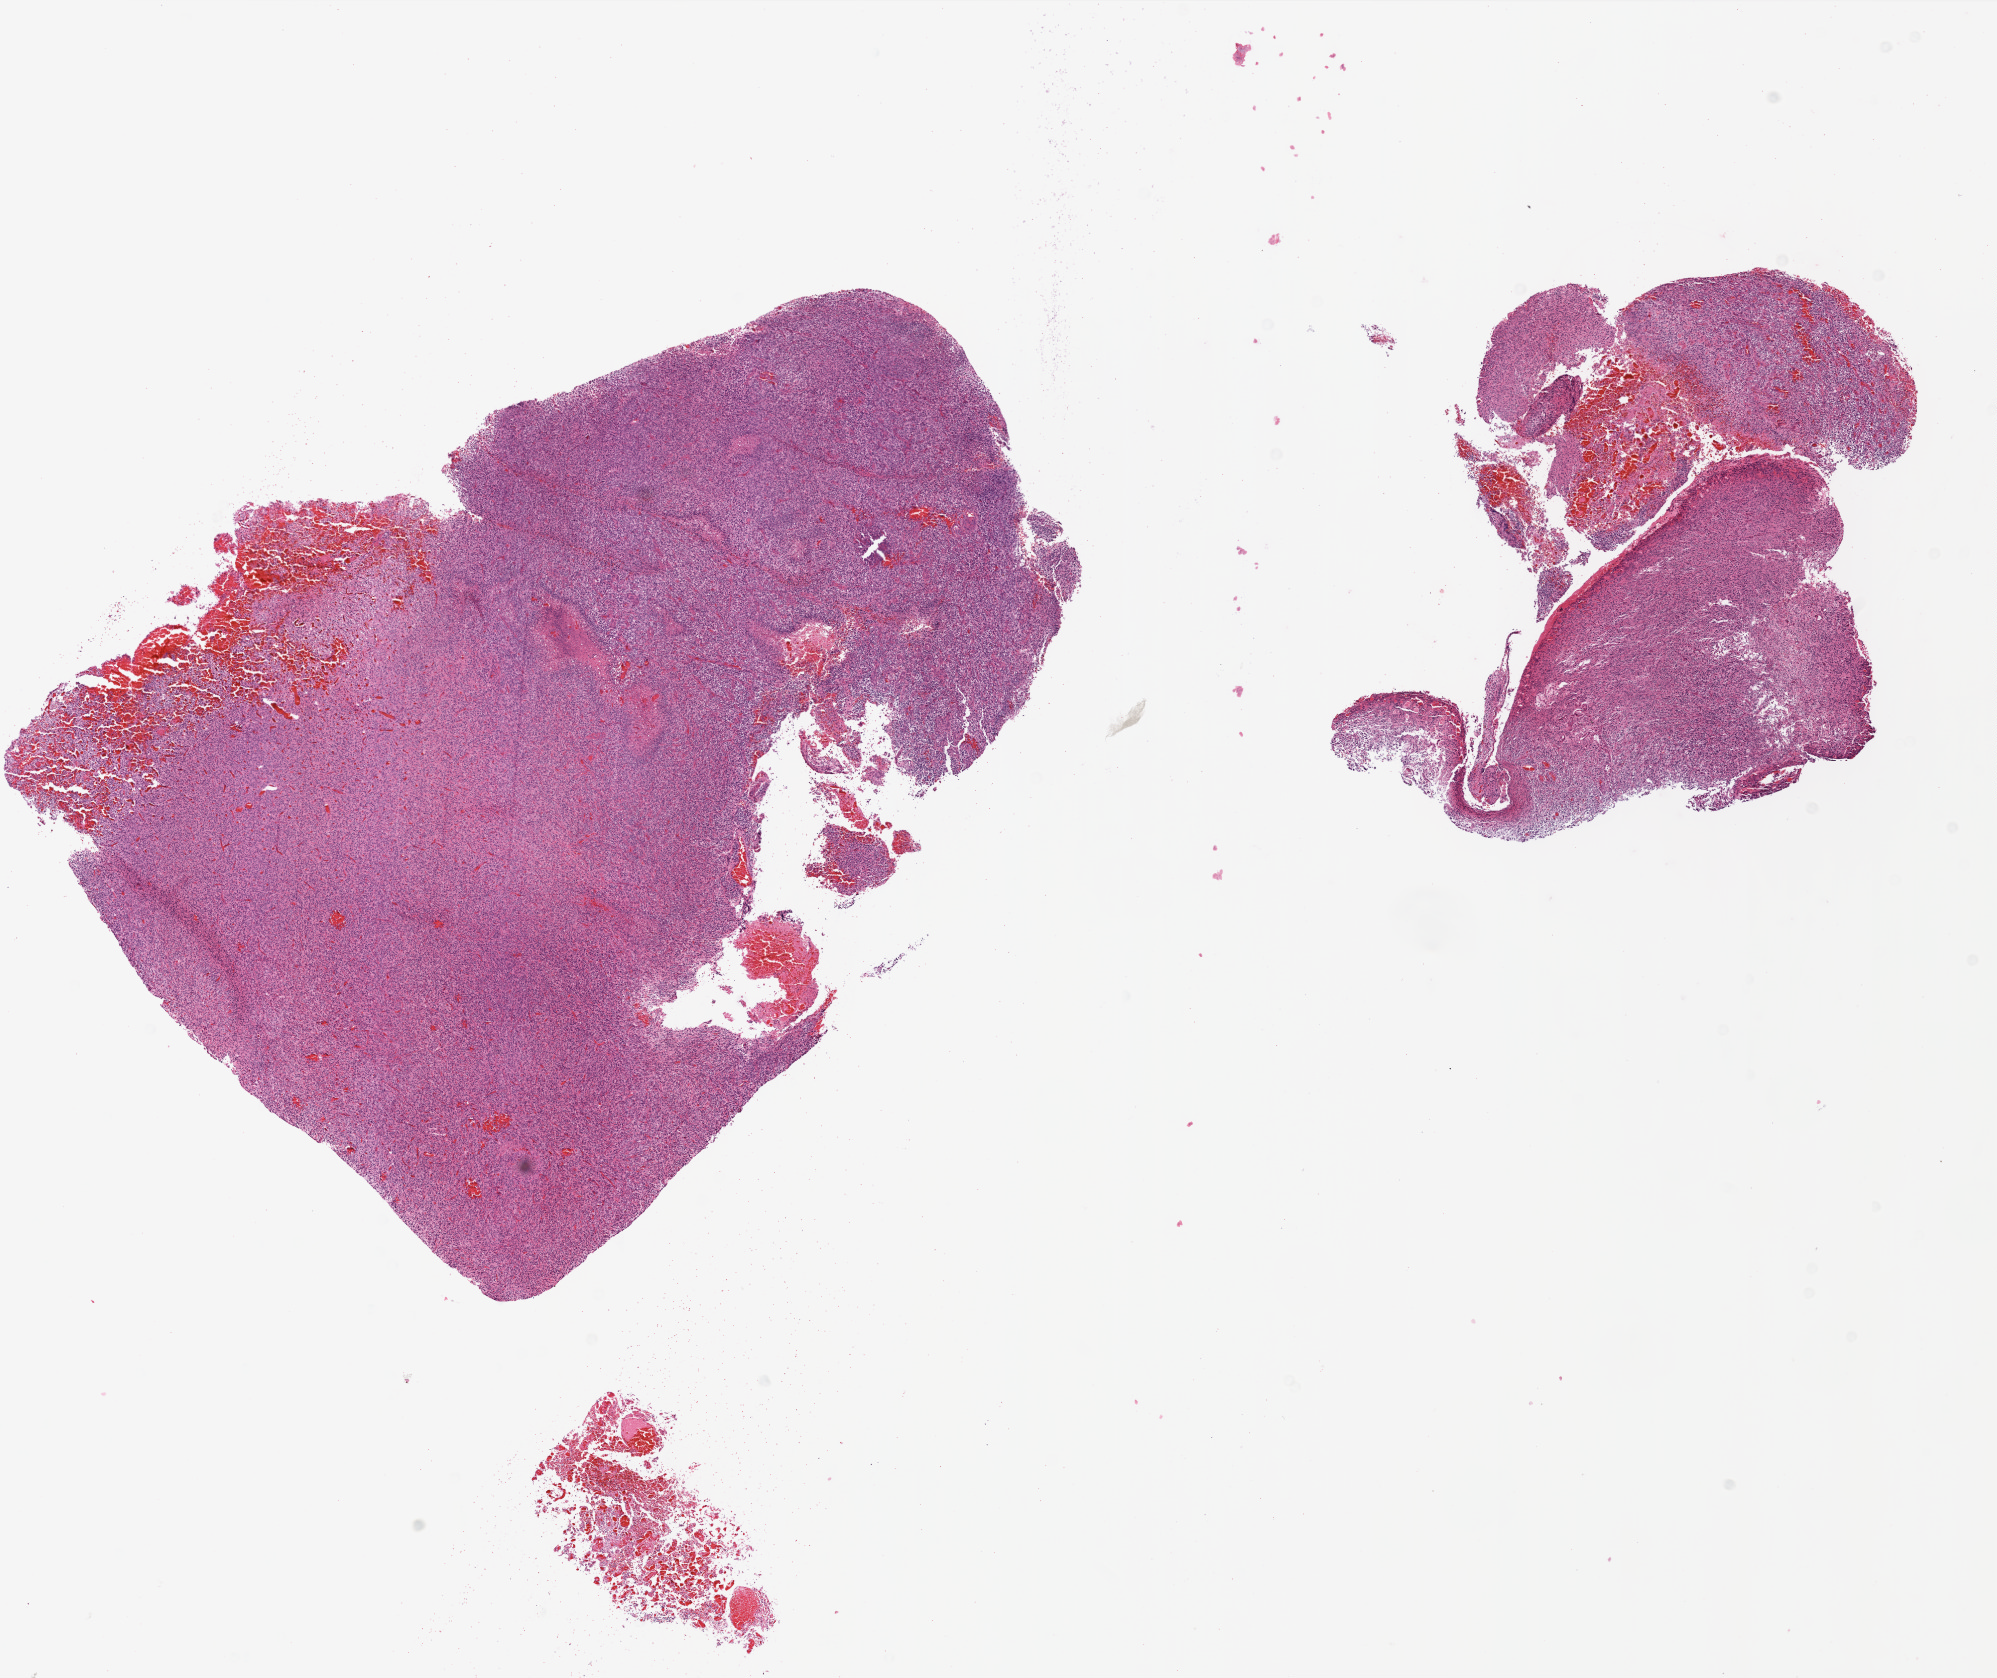
Digitized Hematoxylin and eosin (H&E) stained tissue section (whole slide) — shown as a low-resolution overview of the whole scanned area (about 16.0 x 13.4 mm); FFPE section; primary tumour sample from the brain. Male patient; age at initial diagnosis 47 years.
• histologic diagnosis: Glioblastoma